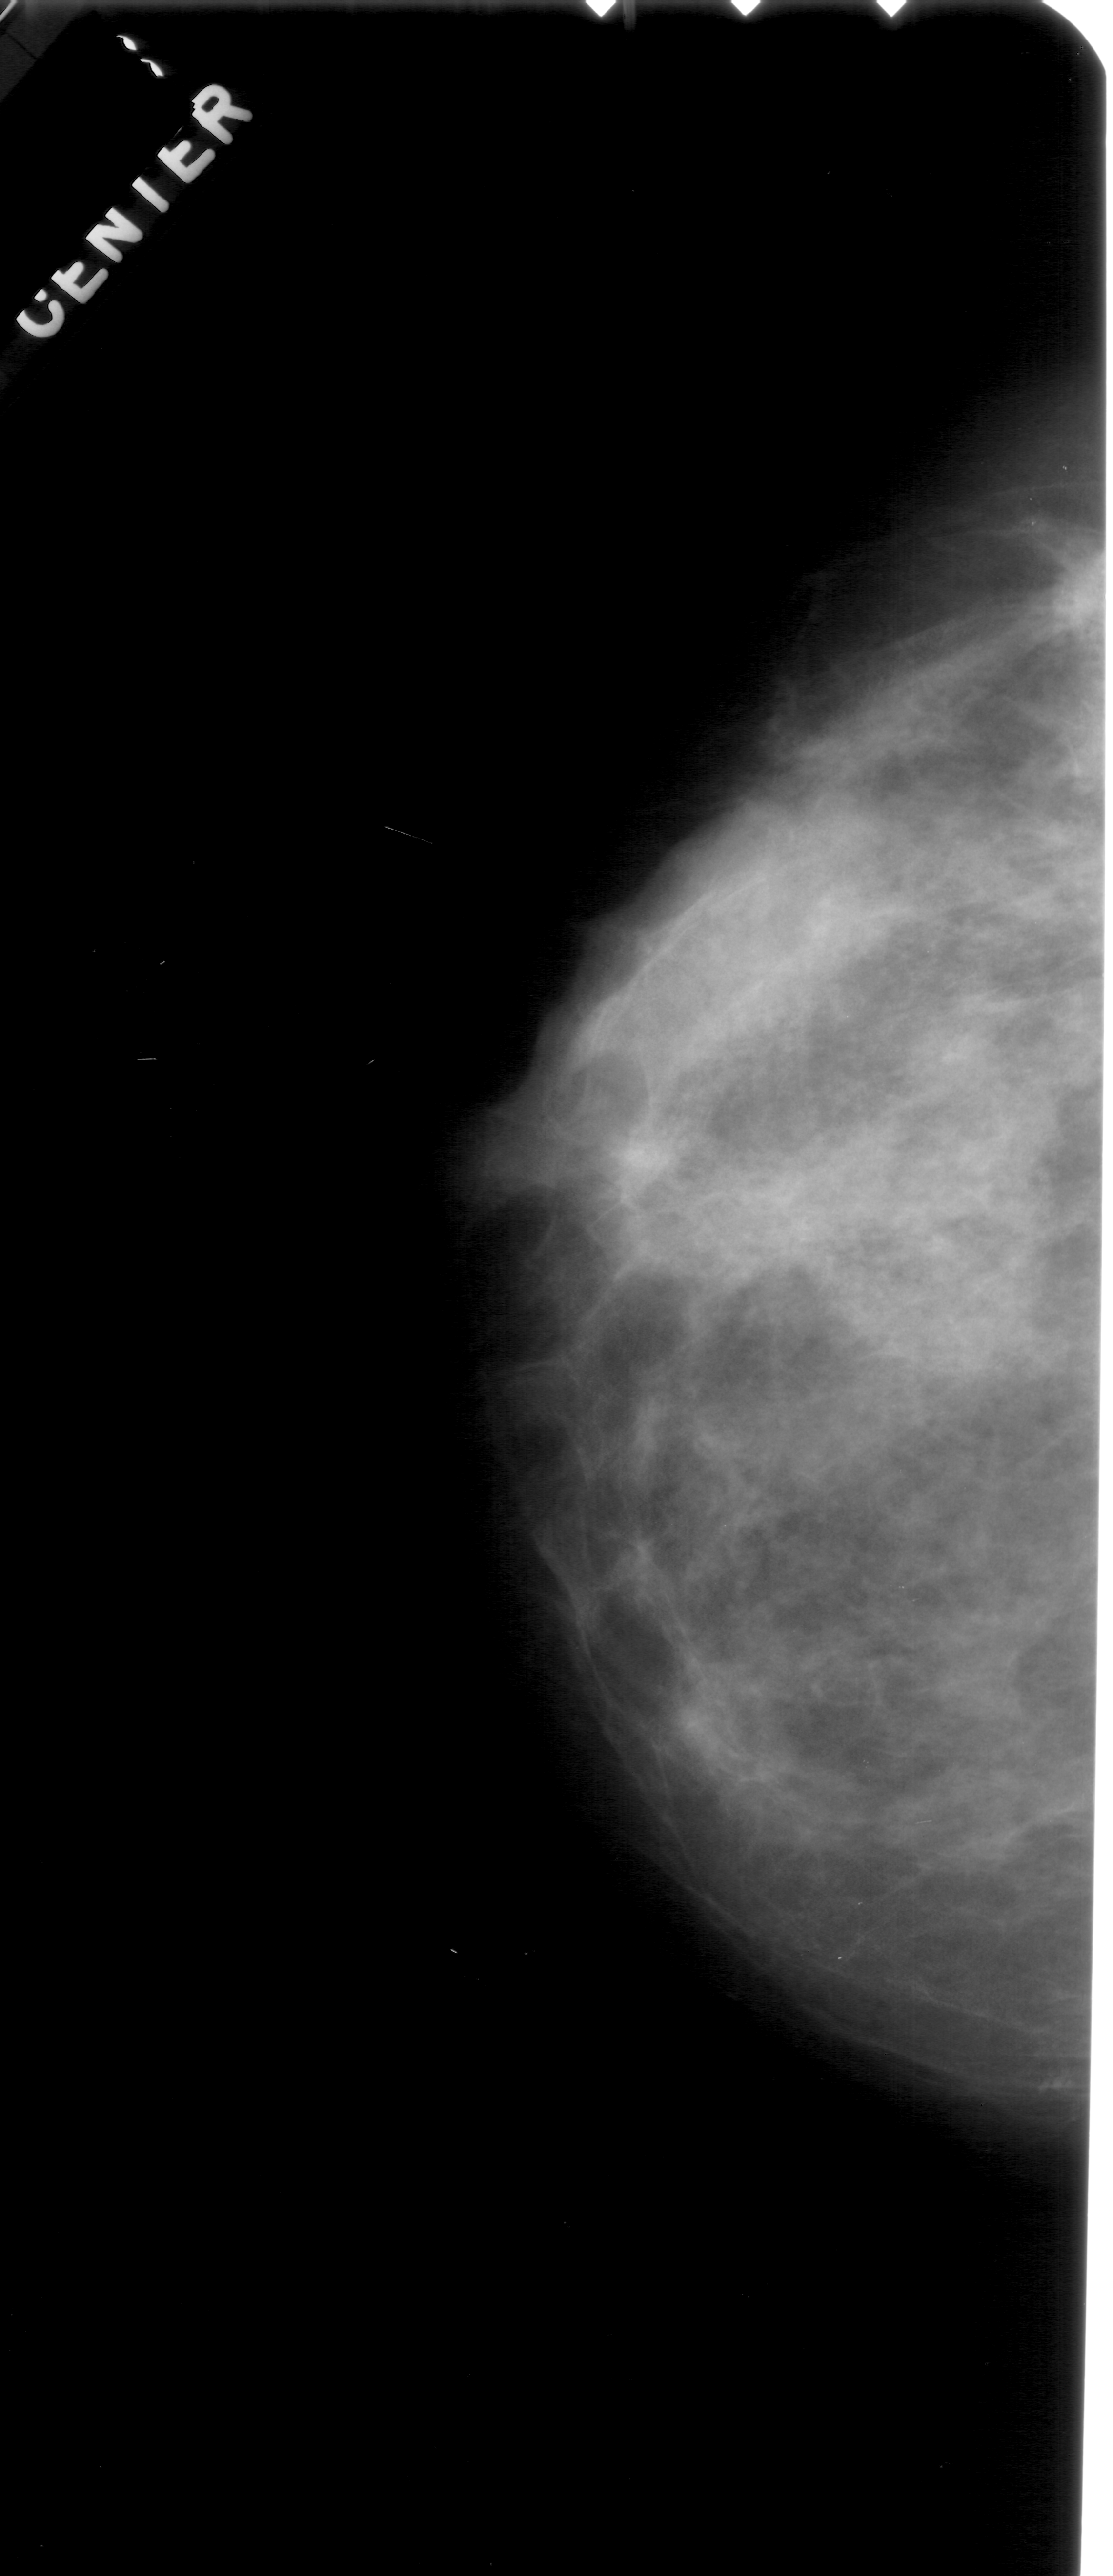
Scanned film-screen mammogram; left breast; CC view; breast composition: extremely dense (BI-RADS density category 4 of 4).
Radiologist-marked abnormalities on this image: mass, shape irregular, margins spiculated; BI-RADS assessment category 4; pathology (as recorded): malignant.